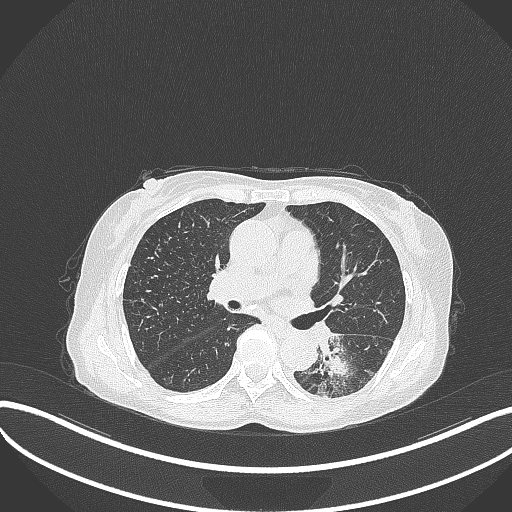
Chest CT, one axial slice. Position 177 of 370 along the scan axis. Reconstruction kernel B70f. Lung window (W 1500 / L -600 HU). 1 mm slice thickness. 512 × 512 image matrix. Female patient, age 78 years. From the clinical record (not read from this slice): clinical TNM (as recorded): T3 N0 M1.
Structures marked on this image (bounding box drawn by a radiologist):
- lung tumour (recorded histology: squamous cell carcinoma): box from (x=314, y=334) to (x=359, y=393) px